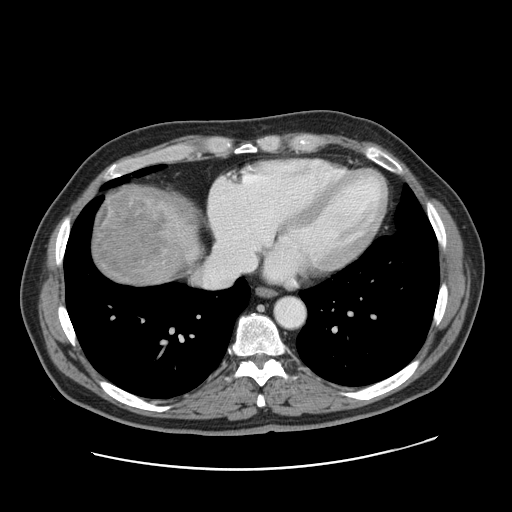
Contrast-enhanced abdominal CT, one axial slice; position 155 of 178 along the scan axis; intravenous contrast given; soft-tissue window (W 400 / L 40 HU); 2.5 mm slice thickness; 512 × 512 image matrix, field of view 403 × 403 mm. Male patient, age 63 years. Case-level facts recorded for this patient, not image findings: diagnosis: colorectal cancer liver metastases, imaged before liver resection; multiple liver metastases: yes; largest metastasis: 8 cm; disease in both lobes: yes.
Annotated regions visible in this slice (manually delineated by an expert):
- liver: bounding box <90,186,199,287> (left, top, right, bottom; pixels)
- liver metastasis: <95,188,165,286>